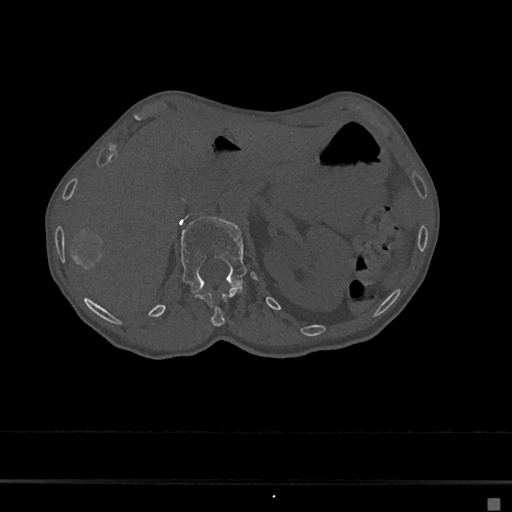
CT including the spine, one axial slice. Position 83 of 797 along the scan axis. 120 kVp. Bone window (W 1800 / L 400 HU). 0.5 mm slice thickness. 512 × 512 image matrix, field of view 360 × 360 mm. Patient: female, 68 years. From the clinical record (not read from this slice): primary cancer: renal.
Outlined on this slice (semi-automatic segmentation, software-assisted and operator-edited):
- L1 vertebra: bounding box <181,217,256,293> (left, top, right, bottom; pixels)
- T12 vertebra: <194,287,243,327>